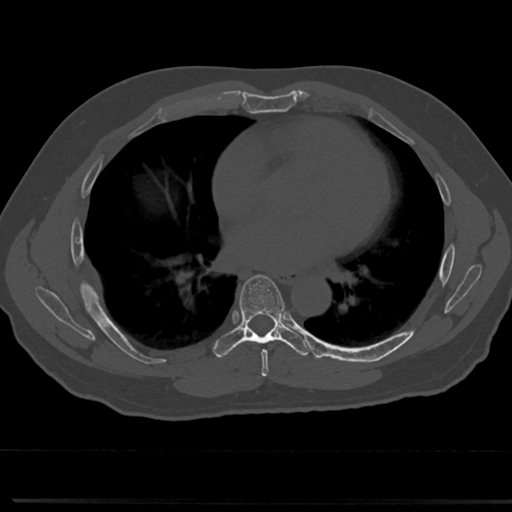
CT including the spine, one axial slice; slice 415 of 817 in the series (ordered by position); reconstruction kernel Br40s/3; 120 kVp; bone window (W 1800 / L 400 HU); 512 × 512 image matrix, field of view 355 × 355 mm. Patient: male, 61 years. From the clinical record (not read from this slice): primary cancer: prostate.
Annotated regions visible in this slice (semi-automatic segmentation, software-assisted and operator-edited):
- T6 vertebra: bounding box <243,281,283,363> (left, top, right, bottom; pixels)
- T7 vertebra: <223,275,286,349>